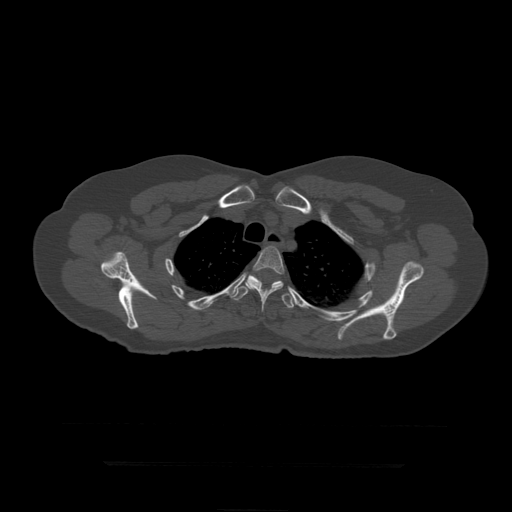
CT including the spine, one axial slice. Slice 345 of 399 in the series (ordered by position). Reconstruction kernel STANDARD. Bone window (W 1800 / L 400 HU). 1.25 mm slice thickness. 512 × 512 image matrix, field of view 450 × 450 mm. Patient age 41 years. From the clinical record (not read from this slice): primary cancer: breast.
Structures marked on this image (semi-automatic segmentation, software-assisted and operator-edited):
- T4 vertebra: bounding box <245,246,285,312> (left, top, right, bottom; pixels)
- T5 vertebra: <231,275,296,308>